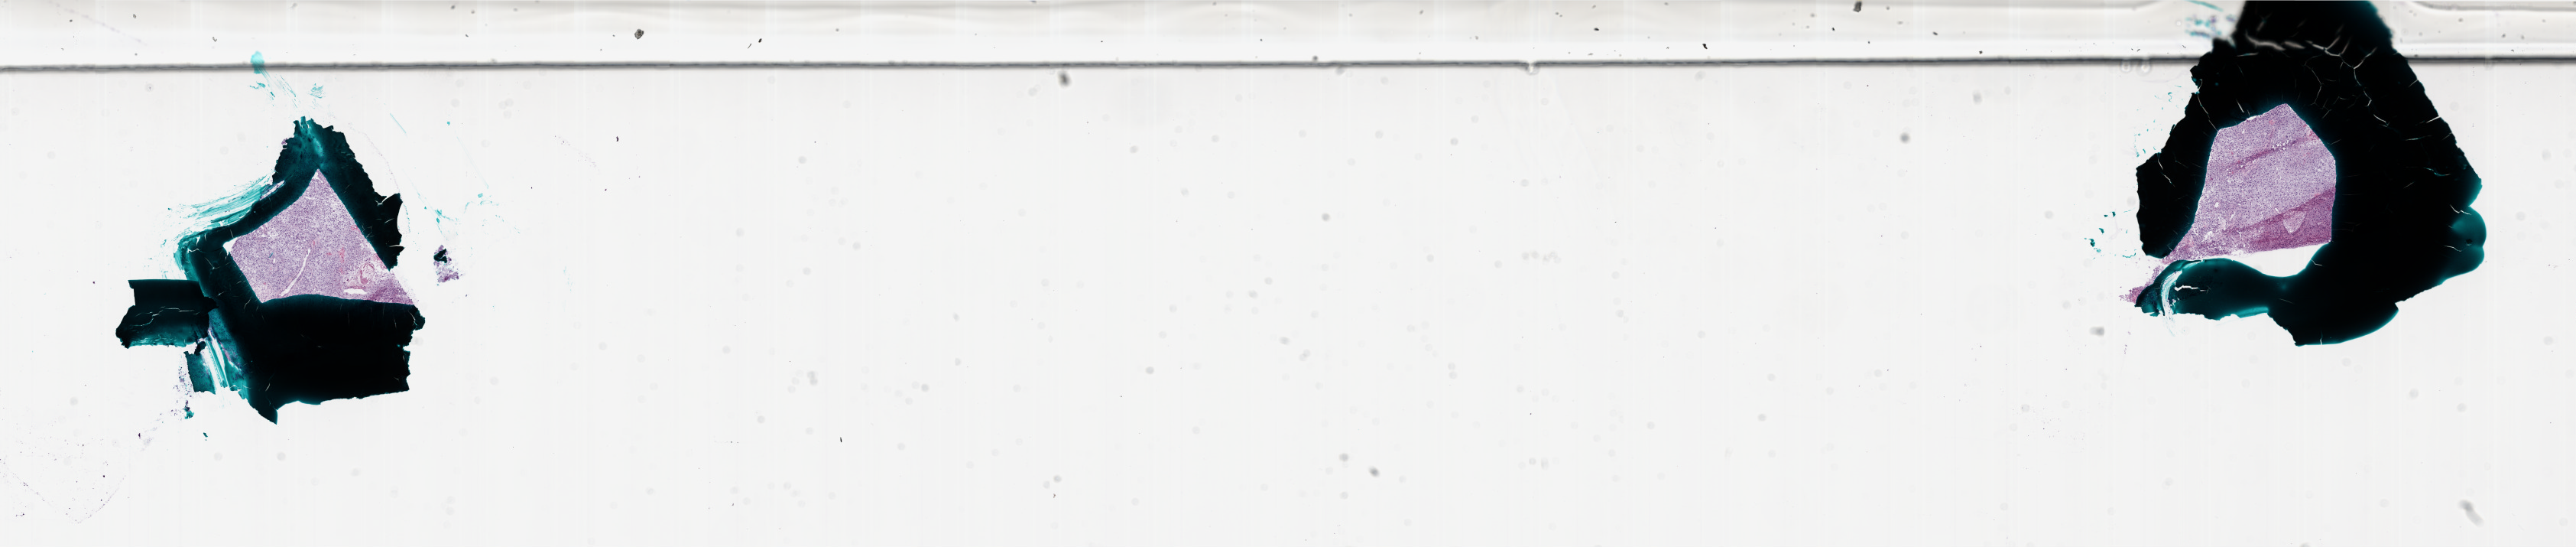
Whole-slide histology image, H&E — a low-resolution overview of the entire scanned area, about 27.0 x 5.7 mm (acquisition: 20x scan), frozen section from the bottom of the tissue portion, brain, primary tumour sample. Female patient; age at initial diagnosis 51 years. Composition of this section per pathologist review: tumour cells 100%, tumour nuclei 98%, normal cells 0%, stromal cells 0%, necrosis 0%.
Diagnosis: Glioblastoma.